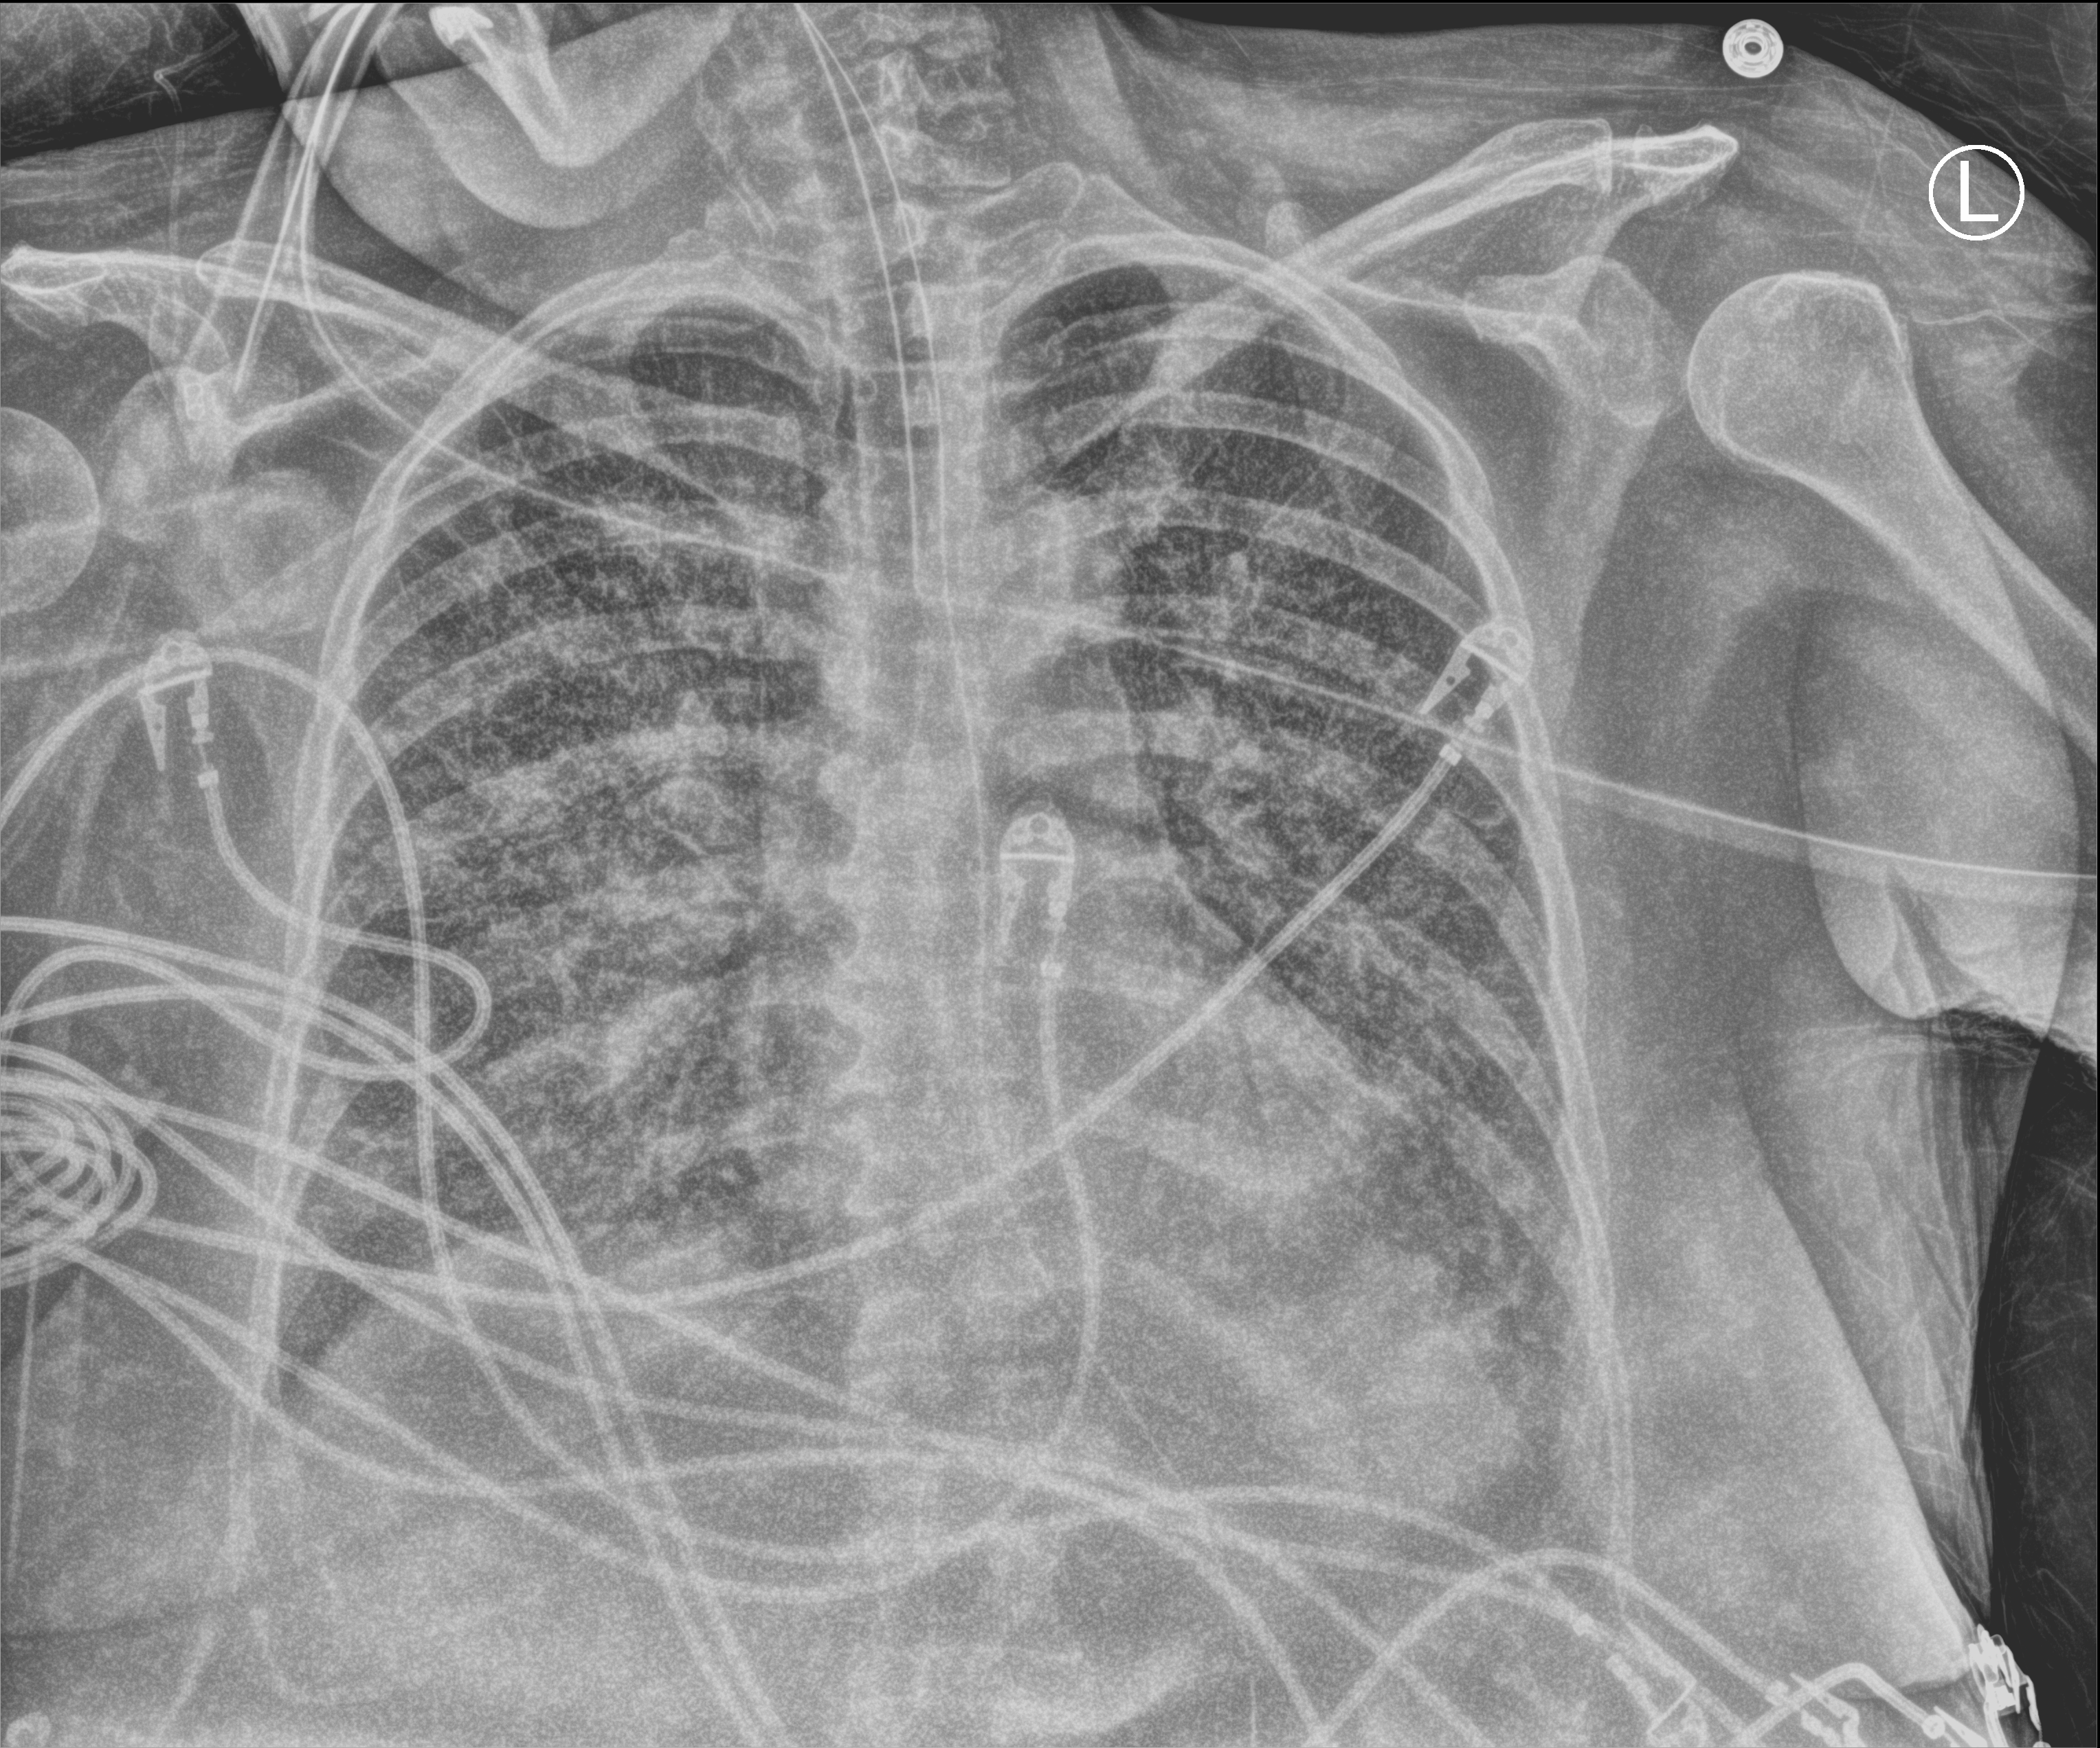
Portable chest radiograph; anteroposterior (AP) projection. Female patient hospitalised with COVID-19, age 60–74 years.
Hospital-stay facts (about this admission, not read from this image; timing relative to this image not recorded): admitted to intensive care during this hospital stay: yes; hypertension (admission record): no.